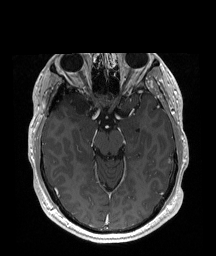
Brain MRI from a brain-tumour surgery series, one axial slice; slice 121 of 192 in the series (ordered by position); T1-weighted post-contrast; 216 × 256 image matrix. From the clinical record (not read from this slice): histopathology: Astrocytoma; WHO grade: 2; IDH mutation: yes.
Structures marked on this image (expert manual segmentation):
- tumour: bounding box (x1, y1, x2, y2) in pixels: (68, 92, 90, 124)